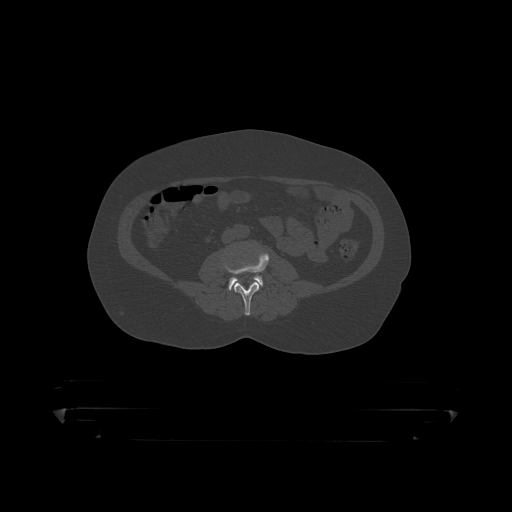
CT including the spine, one axial slice; position 81 of 390 along the scan axis; reconstruction kernel STANDARD; 120 kVp; bone window (W 1800 / L 400 HU); 1.25 mm slice thickness; 512 × 512 image matrix, field of view 650 × 650 mm. Male patient, age 60 years. From the clinical record (not read from this slice): primary cancer: prostate.
Outlined on this slice (semi-automatically segmented with operator editing):
- L3 vertebra: bounding box [x1, y1, x2, y2] px = [223, 249, 269, 316]
- L4 vertebra: [229, 275, 263, 291]